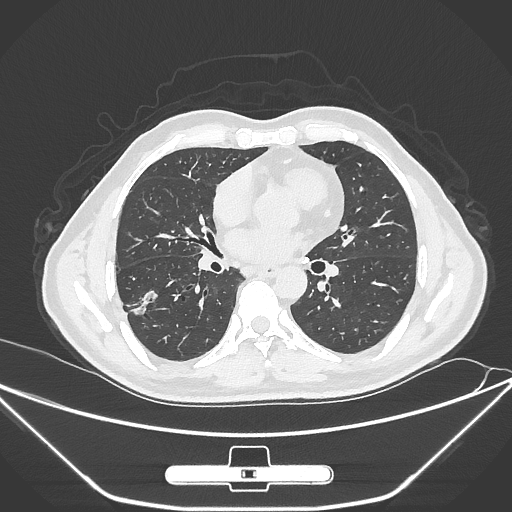
Chest CT, one axial slice; slice 142 of 310 in the series (ordered by position); lung window (W 1500 / L -600 HU); 1 mm slice thickness; 512 × 512 image matrix, field of view 398 × 398 mm. Male patient, age 71 years. From the clinical record (not read from this slice): clinical TNM (as recorded): T1c N0 M0; histopathological grade: G2.
Structures marked on this image (rectangle marked by the reading radiologist):
- lung tumour (recorded histology: adenocarcinoma): bounding box [x1, y1, x2, y2] px = [127, 282, 164, 328]